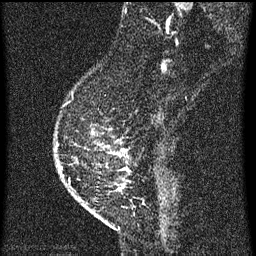
Breast MRI (dynamic contrast-enhanced), one sagittal slice. Slice 16 of 60 in the series (ordered by position). Dynamic contrast-enhanced series, image 2 of 3 at this slice position (ordered by acquisition). 1.5 T. TE 4.2 ms, TR 8 ms. 256 × 256 image matrix, field of view 180 × 180 mm. Female patient, age 47 years.
Annotated regions visible in this slice (semi-automatically segmented with operator editing):
- analysis volume of interest (the breast-tissue region the enhancement analysis was run in; not a lesion): bounding box [x1, y1, x2, y2] px = [56, 84, 133, 203]
- tumour enhancement mask (voxels above the 70 % enhancement threshold inside the analysis volume of interest): [59, 154, 125, 185]